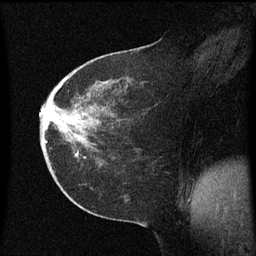
Breast MRI (dynamic contrast-enhanced), one sagittal slice; slice 28 of 60 in the series (ordered by position); dynamic contrast-enhanced series, image 2 of 3 at this slice position (ordered by acquisition); 1.5 T; TE 4.2 ms, TR 8.4 ms; 256 × 256 image matrix. Patient: female, 38 years. Case-level facts recorded for this patient, not image findings: setting: breast cancer imaged before/during neoadjuvant chemotherapy; receptor status: HER2-positive.
Outlined on this slice (semi-automatic segmentation, software-assisted and operator-edited):
- analysis volume of interest (the breast-tissue region the enhancement analysis was run in; not a lesion): box from (x=40, y=50) to (x=145, y=185) px
- tumour enhancement mask (voxels above the 70 % enhancement threshold inside the analysis volume of interest): (x=41, y=112)–(x=78, y=155)